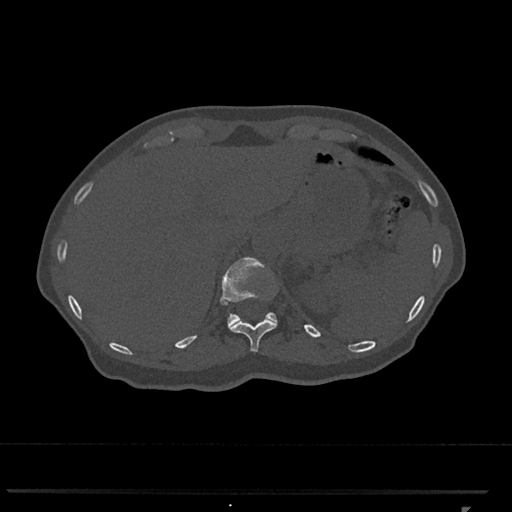
CT including the spine, one axial slice; position 497 of 793 along the scan axis; 120 kVp; bone window (W 1800 / L 400 HU); 0.5 mm slice thickness; 512 × 512 image matrix, field of view 380 × 380 mm. Patient: female, 62 years. From the clinical record (not read from this slice): primary cancer: renal.
Structures marked on this image (semi-automatic segmentation, software-assisted and operator-edited):
- T11 vertebra: bounding box <228,319,278,352> (left, top, right, bottom; pixels)
- T12 vertebra: <220,257,277,326>